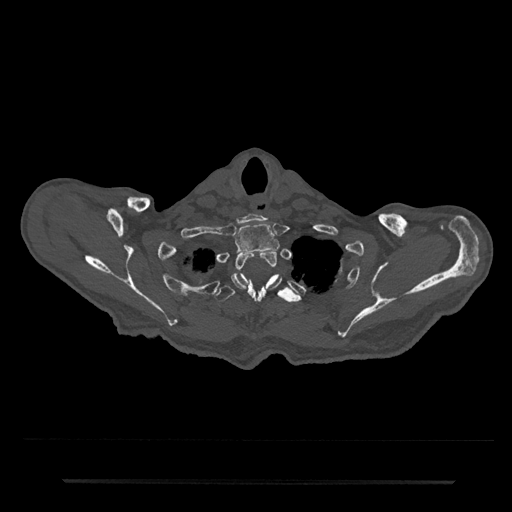
CT including the spine, one axial slice. Slice 688 of 797 in the series (ordered by position). Reconstruction kernel Br40s/3. 120 kVp. Bone window (W 1800 / L 400 HU). 512 × 512 image matrix, field of view 427 × 427 mm. Patient: male, 74 years. From the clinical record (not read from this slice): primary cancer: prostate.
Outlined on this slice (semi-automatically segmented with operator editing):
- T1 vertebra: bounding box (x1, y1, x2, y2) in pixels: (235, 223, 280, 253)
- T2 vertebra: (231, 250, 279, 298)
- T3 vertebra: (215, 273, 301, 338)